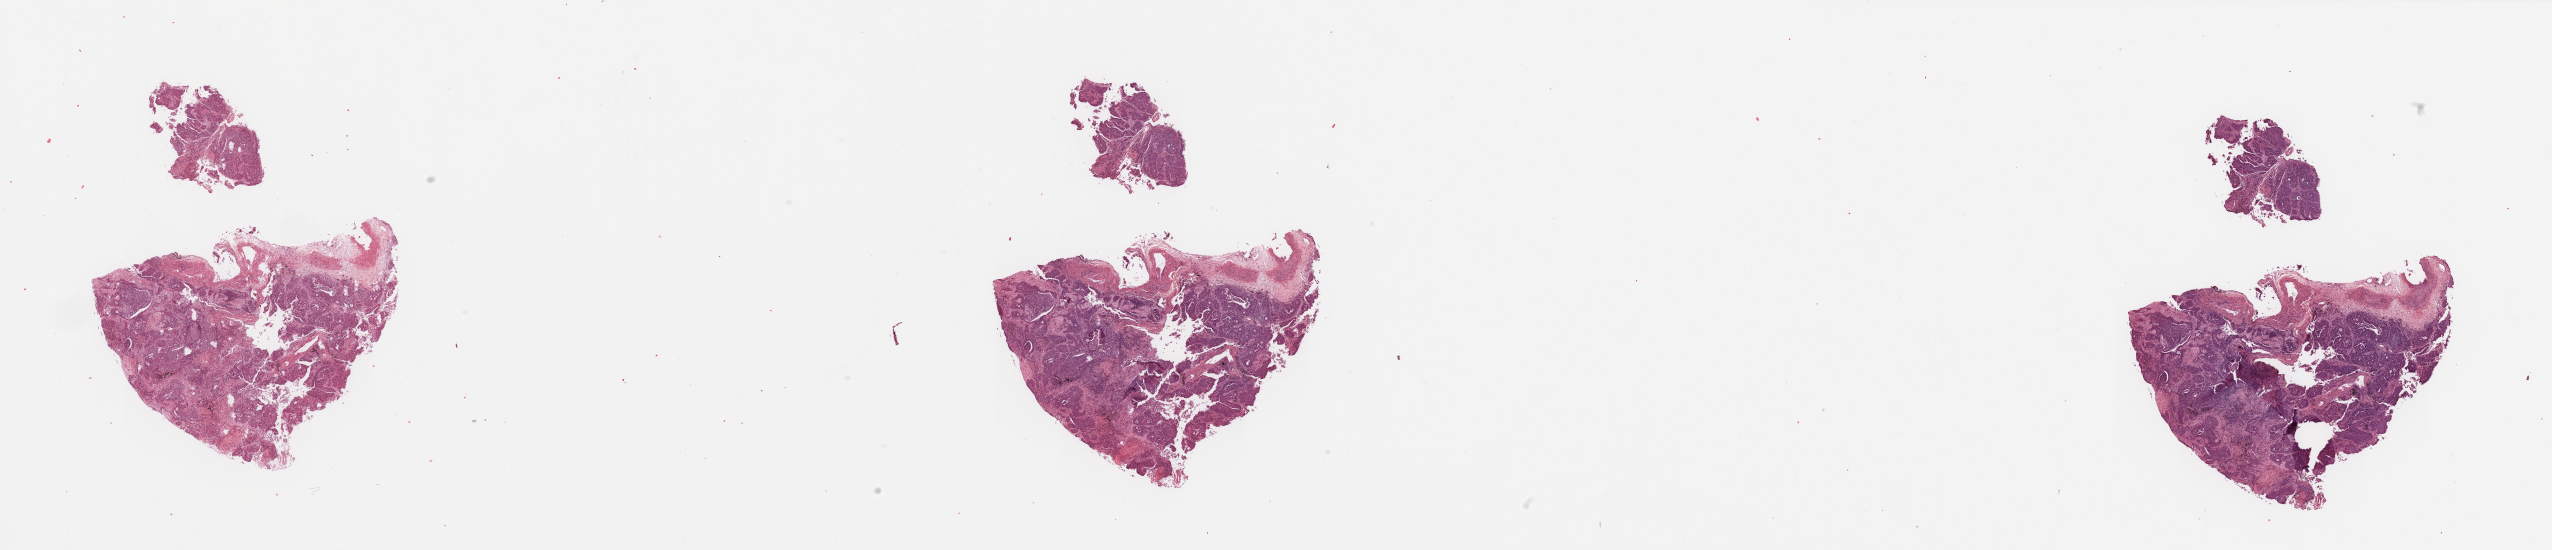
Whole-slide histology image, Hematoxylin and eosin (H&E) stained, low-resolution overview of the scanned area, about 40.4 x 8.7 mm (acquisition: 20x scan). Tumour tissue sample, sampled site: lung. 74-year-old male patient. Histologic grade: G3 (poorly differentiated). Composition of this section per pathologist review: tumour nuclei 75%, necrosis 7%.
Histologic diagnosis: Squamous cell carcinoma, NOS. Primary tumour site (as recorded): right lower lobe. AJCC pathologic stage: IA.